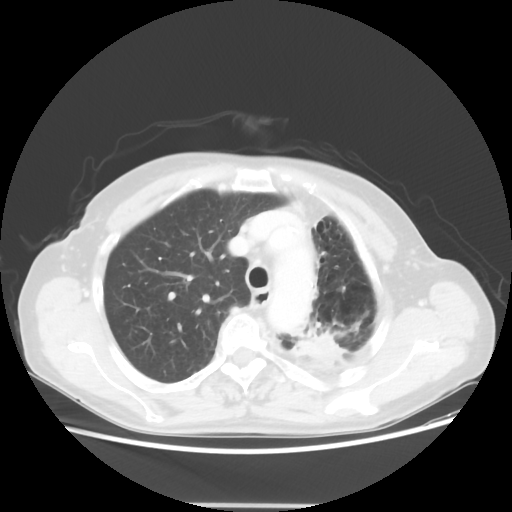
Chest CT, one axial slice. Slice 40 of 56 in the series (ordered by position). Reconstruction kernel STANDARD. 100 kVp. Lung window (W 1500 / L -600 HU). 512 × 512 image matrix, field of view 377 × 377 mm. Patient: female, 63 years. From the clinical record (not read from this slice): clinical TNM (as recorded): T2a N0 M0.
Outlined on this slice (bounding box drawn by a radiologist):
- lung tumour (recorded histology: adenocarcinoma): bounding box [x1, y1, x2, y2] px = [295, 327, 345, 370]